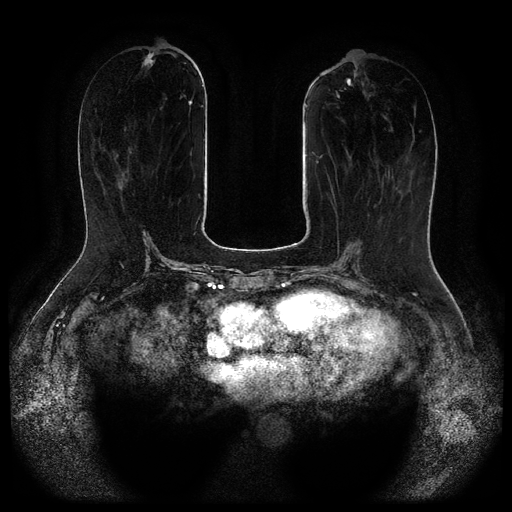
Breast MRI (dynamic contrast-enhanced, multi-phase), one axial slice; position 39 of 116 along the scan axis; dynamic contrast-enhanced series, time point 2 of 5 at this slice position (early post-contrast); 1.5 T; TE 2.6 ms, TR 5.3 ms; 2.1 mm slice thickness; 512 × 512 image matrix, field of view 360 × 360 mm. Patient: female, 65 years.
Structures marked on this image (semi-automatically segmented with operator editing):
- breast lesion (labelled 'tumour' in the annotation; benign lesions carry a separate 'benign' label): bounding box [x1, y1, x2, y2] px = [144, 53, 153, 66]